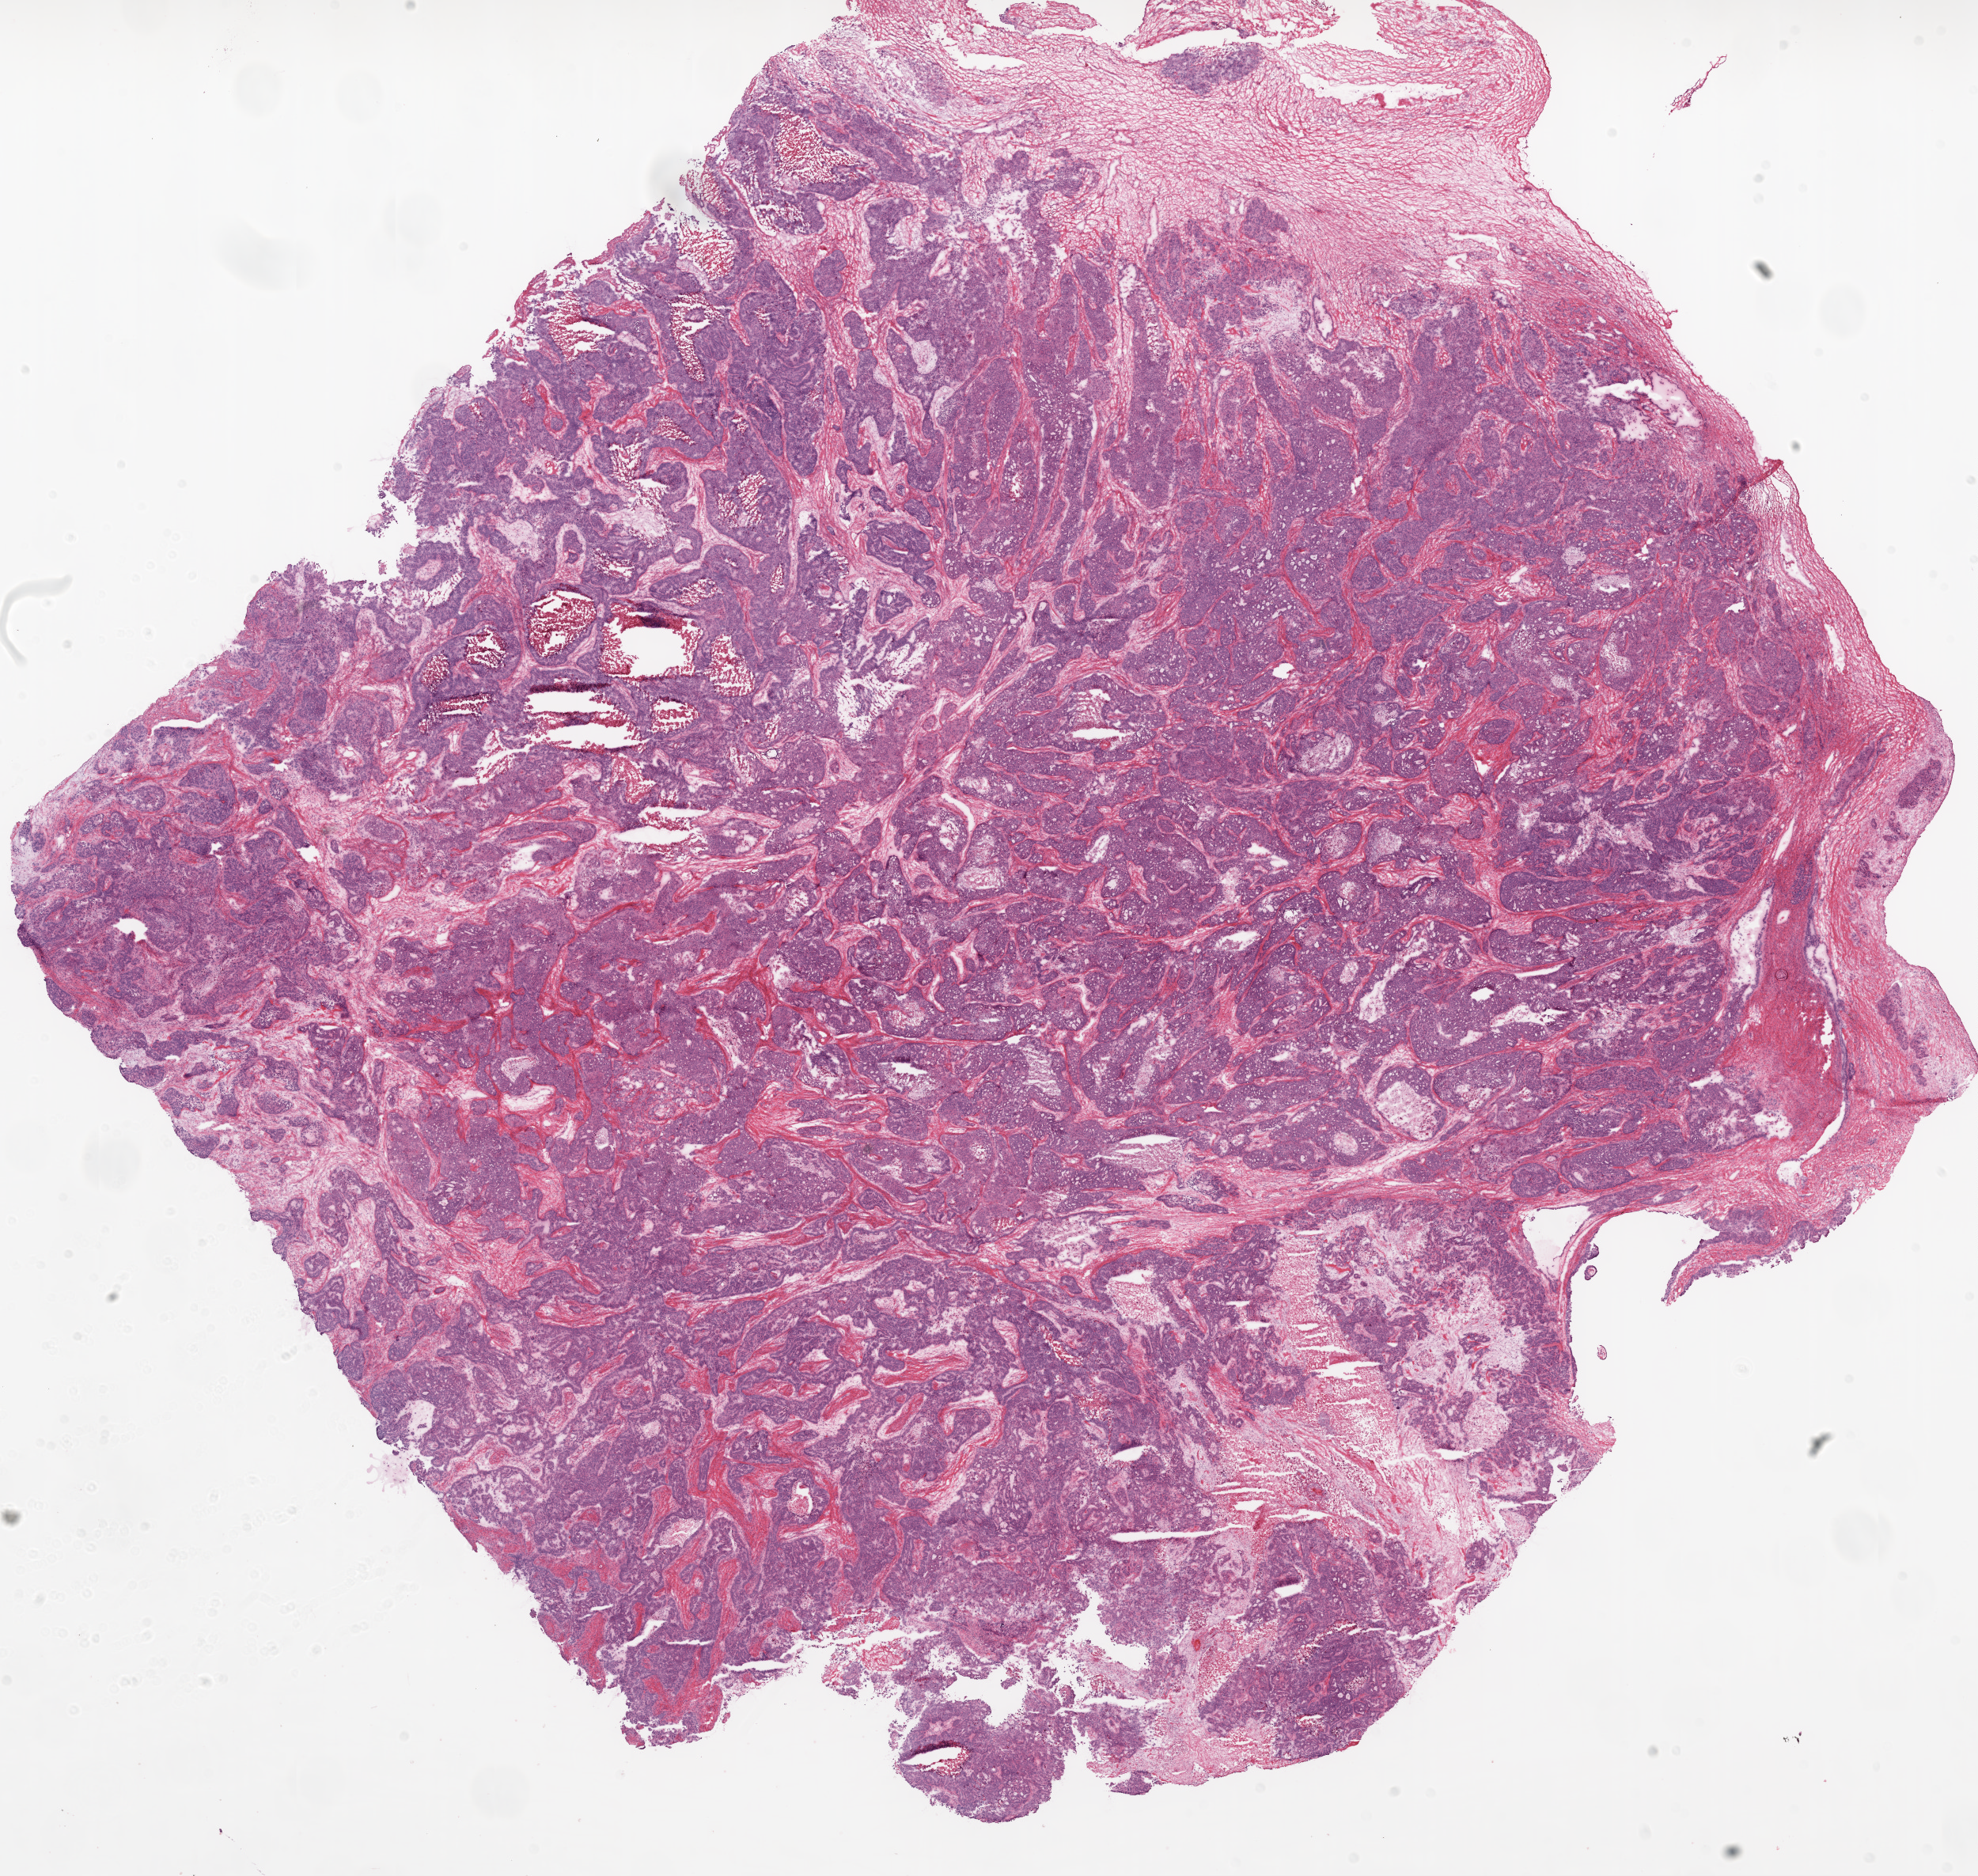
Whole-slide histology image, H&E, low-resolution overview of the scanned area, about 20.1 x 19.0 mm. Frozen section from the top of the tissue portion. Primary tumour sample from the ovary. Female, age 73 years at initial diagnosis. Pathologist review of this section (percent, as recorded): tumour cells 90%, tumour nuclei 95%.
Pathologic diagnosis: Serous cystadenocarcinoma, NOS.